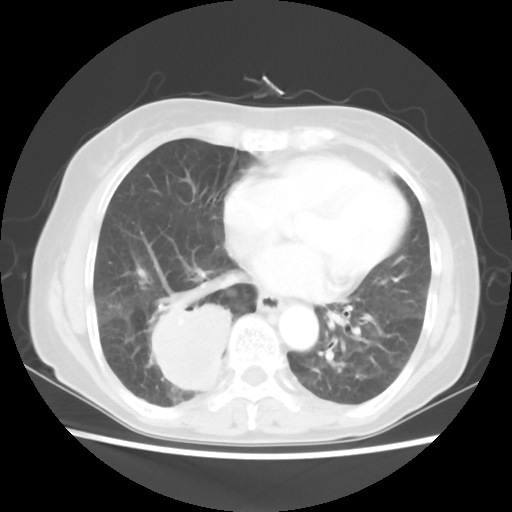
Chest CT, one axial slice. Slice 24 of 56 in the series (ordered by position). Reconstruction kernel STANDARD. Lung window (W 1500 / L -600 HU). 5 mm slice thickness. 512 × 512 image matrix, field of view 332 × 332 mm. Patient: female, 66 years. Case-level facts recorded for this patient, not image findings: clinical TNM (as recorded): T2 N3 M0; histopathological grade: G3.
Annotated regions visible in this slice (bounding box drawn by a radiologist):
- lung tumour (recorded histology: small cell carcinoma): bounding box (x1, y1, x2, y2) in pixels: (146, 300, 245, 403)